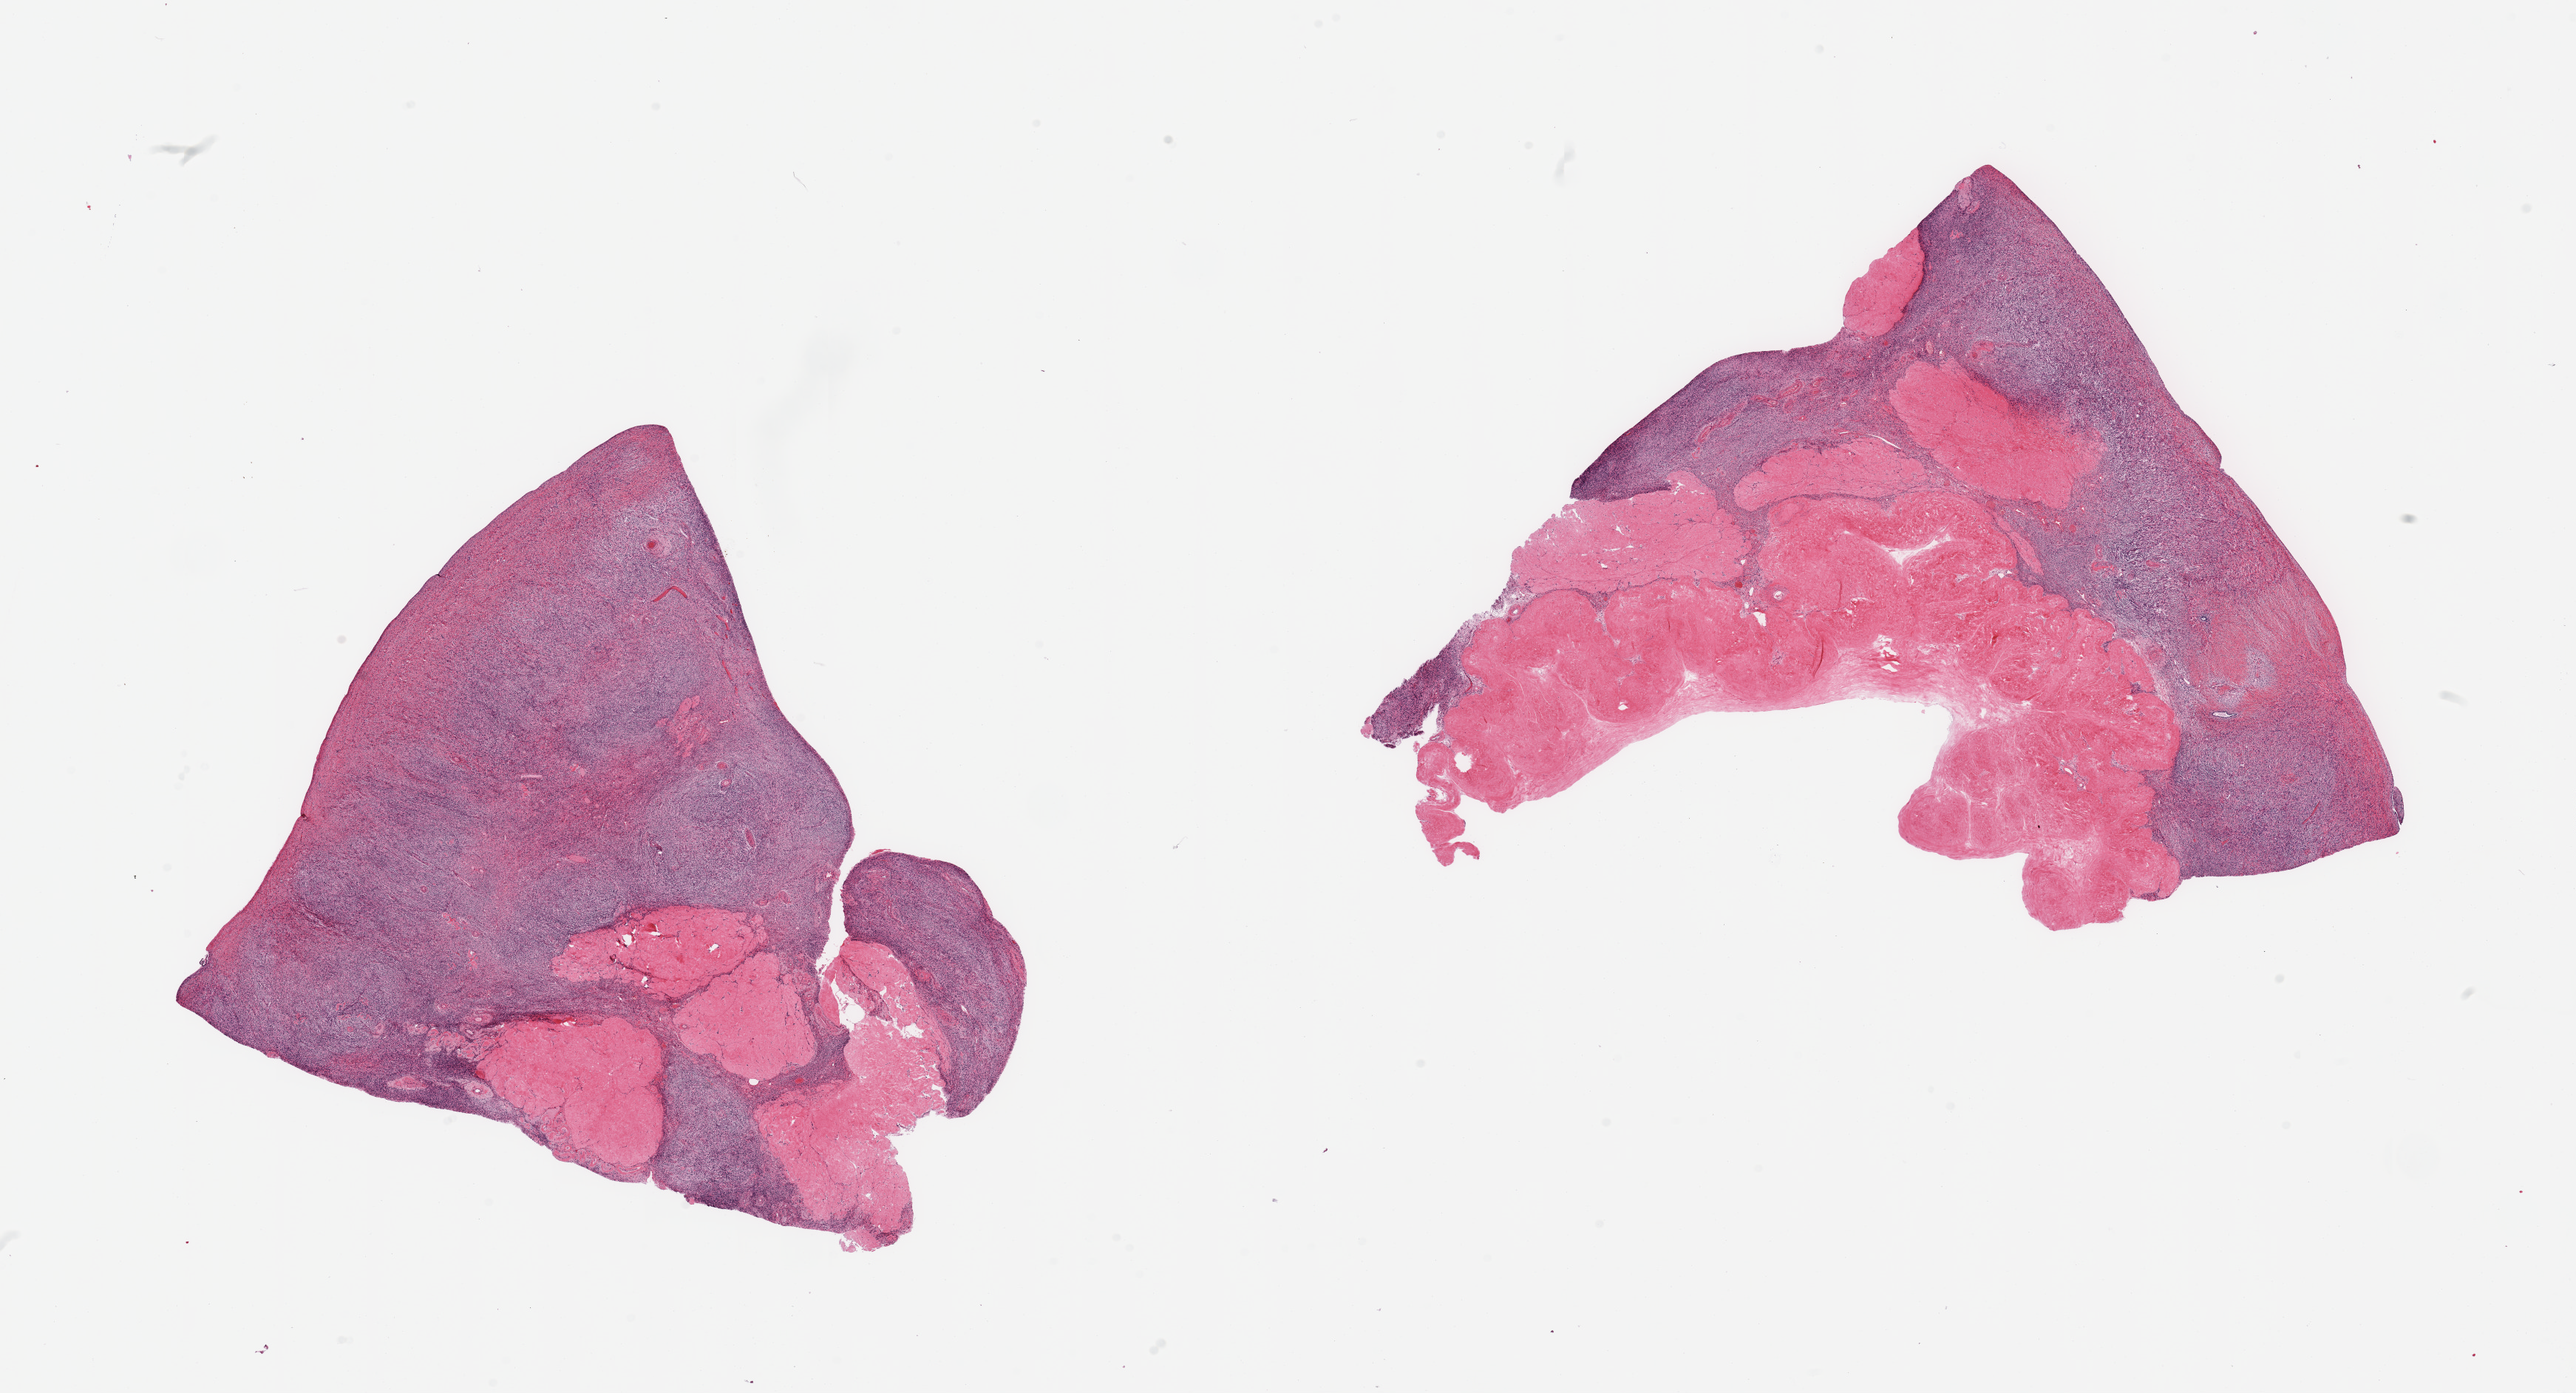
Whole-slide image, hematoxylin and eosin (H&E) stain — whole scanned area (about 27.6 x 14.9 mm) shown as a low-resolution overview, PAXgene-fixed, paraffin-embedded tissue, section of ovary (target tissue), donor tissue sample. Donor: female.
Reviewer comment on this tissue sample: 2 pieces; corpora albicantia.